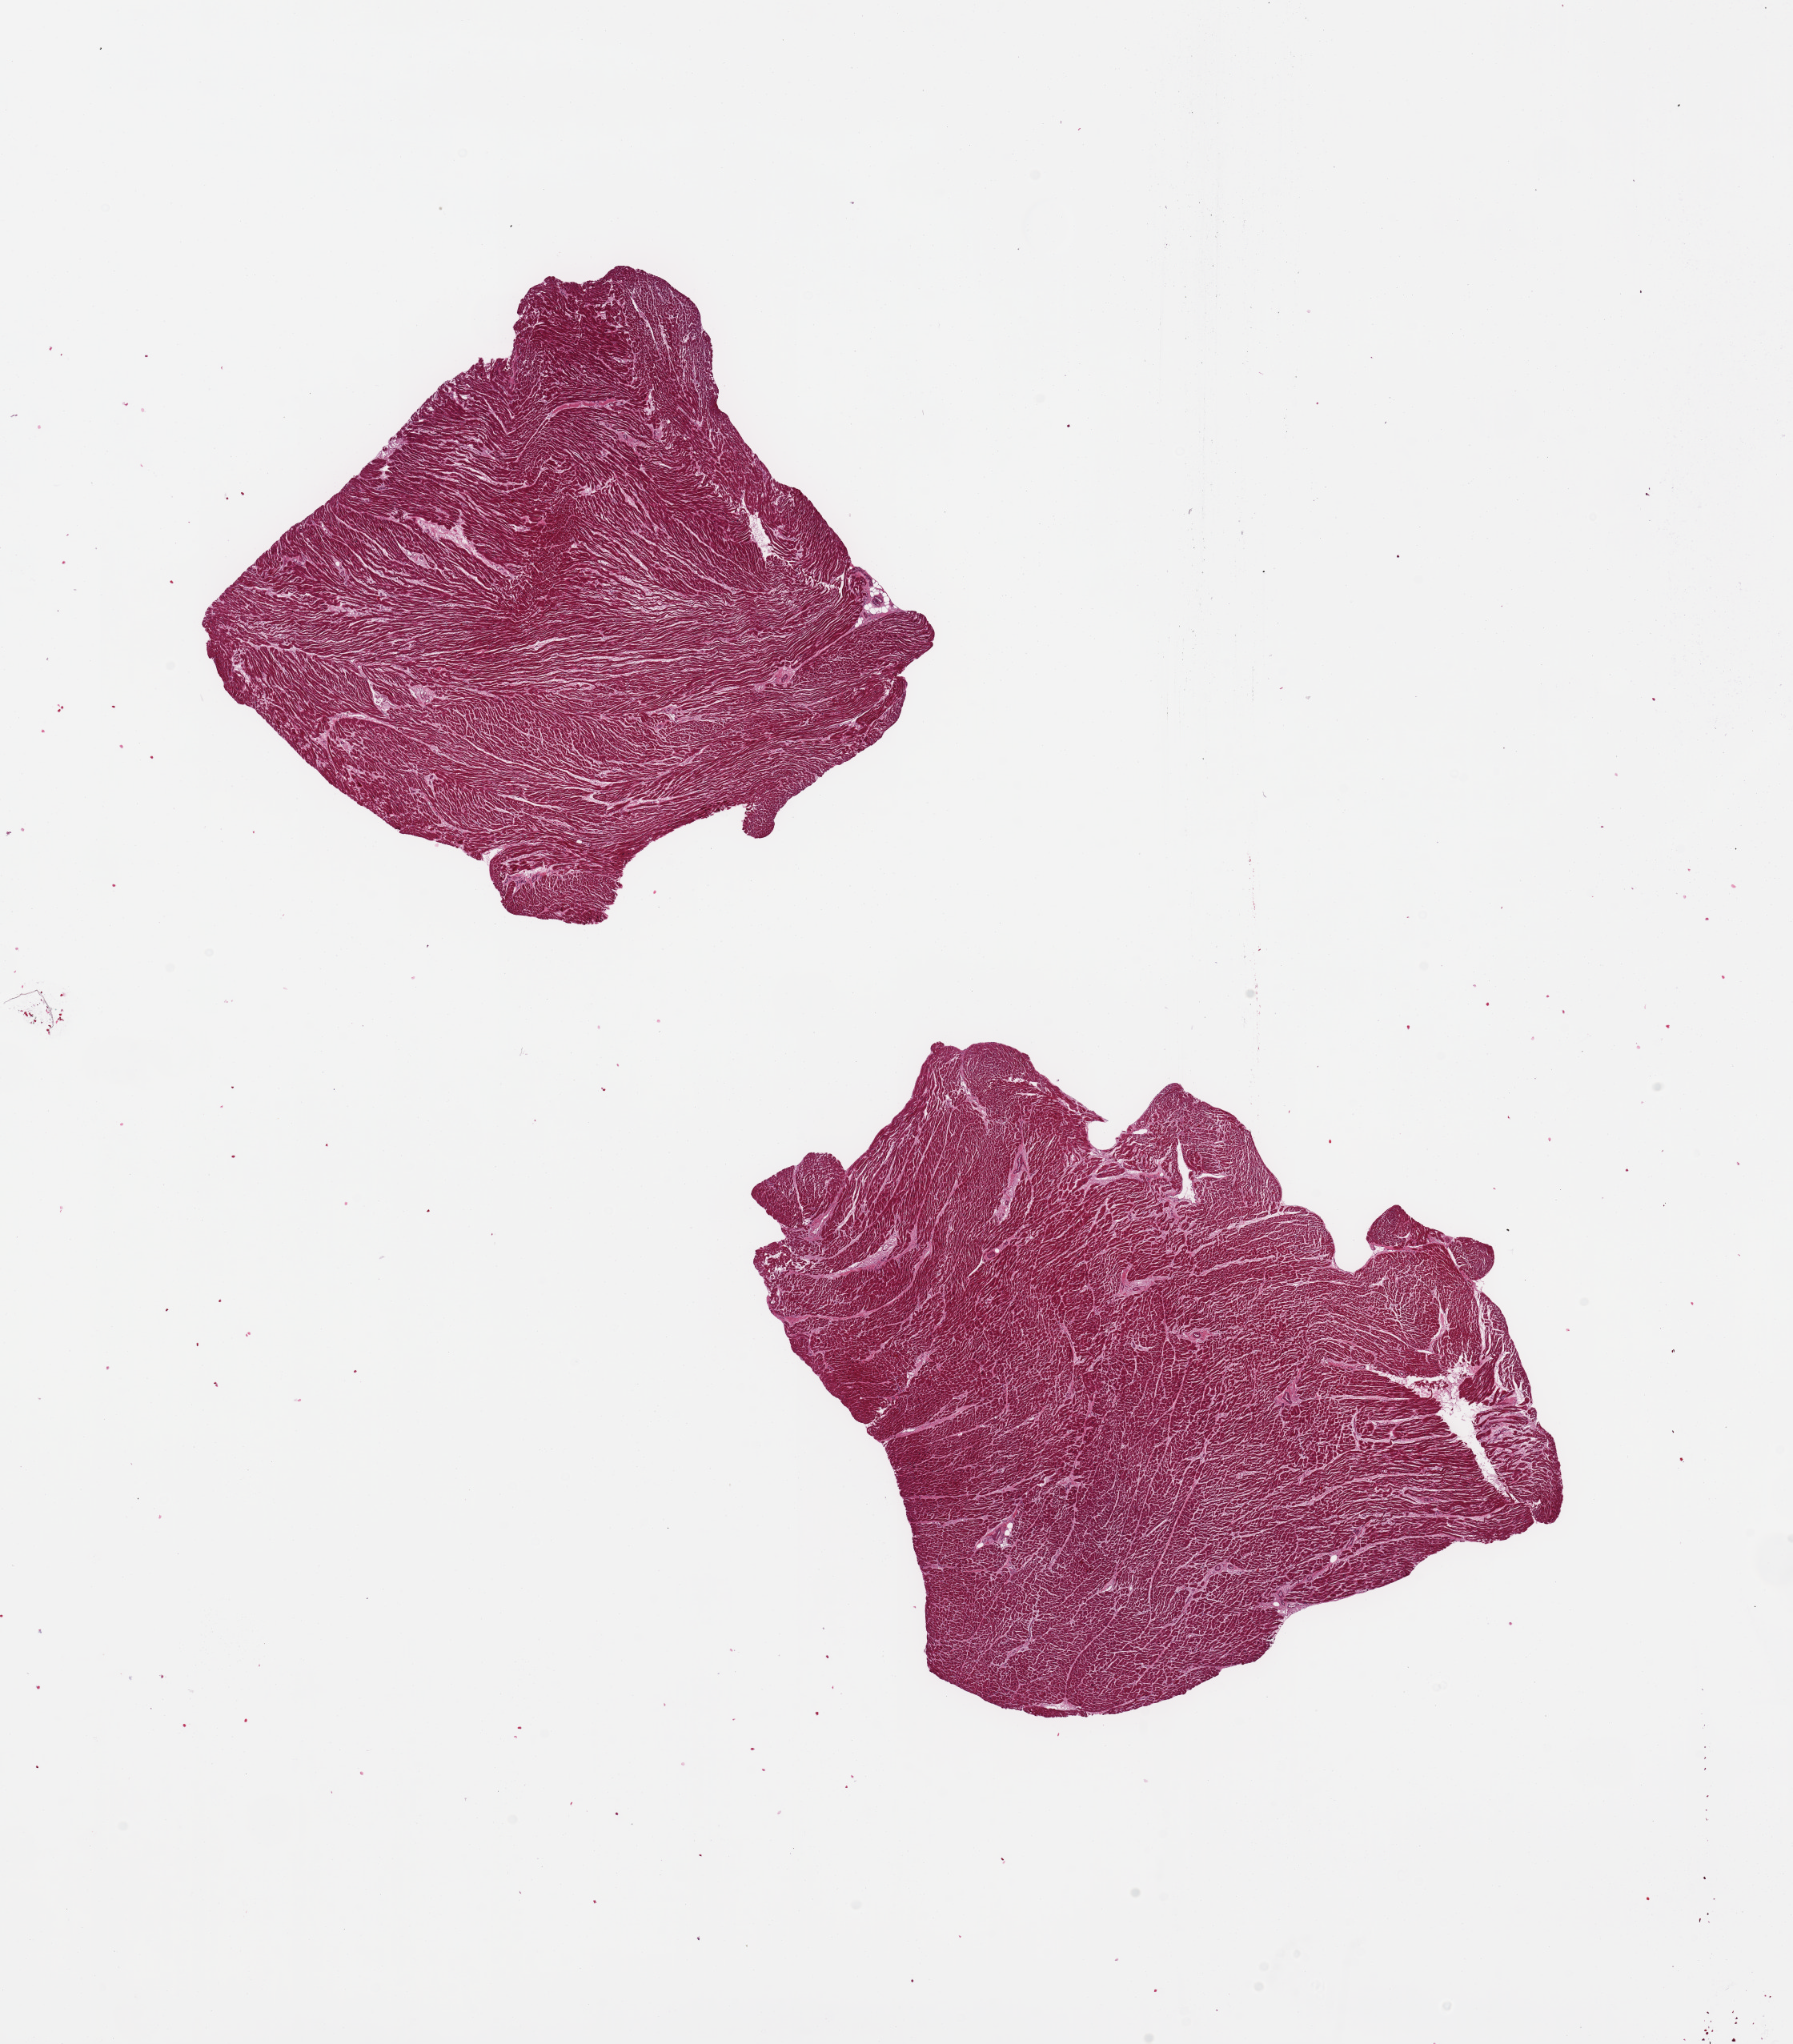
Haematoxylin and eosin whole-slide image — a low-resolution overview of the entire scanned area, about 17.7 x 20.2 mm; PAXgene-fixed, paraffin-embedded tissue; target tissue: heart; tissue donor sample.
Pathologist's review note for this sample: 2 pieces; subtle interstitial fibrosis.